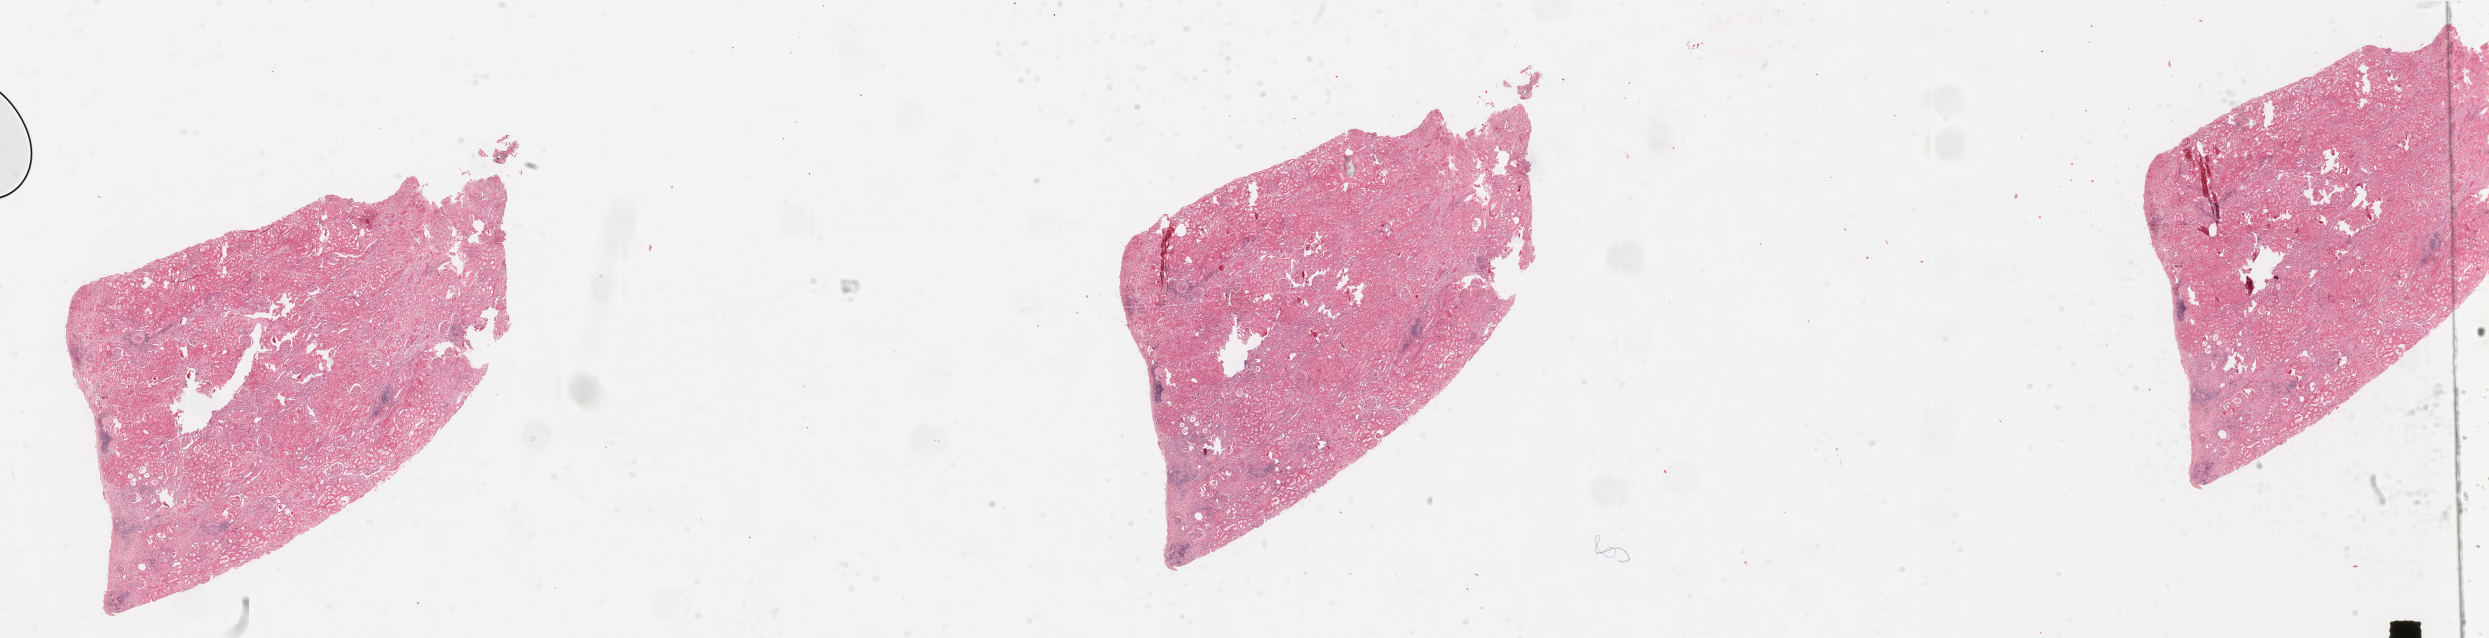
Digitized H&E tissue section (whole slide), shown as a low-resolution overview of the whole scanned area (about 39.4 x 10.1 mm, from a 20x scan), normal (non-tumour) tissue sample, sampled site: kidney. Patient: male, age 69 years.
• this section: normal (non-tumour) tissue from the same patient
• patient diagnosis: Renal cell carcinoma, NOS